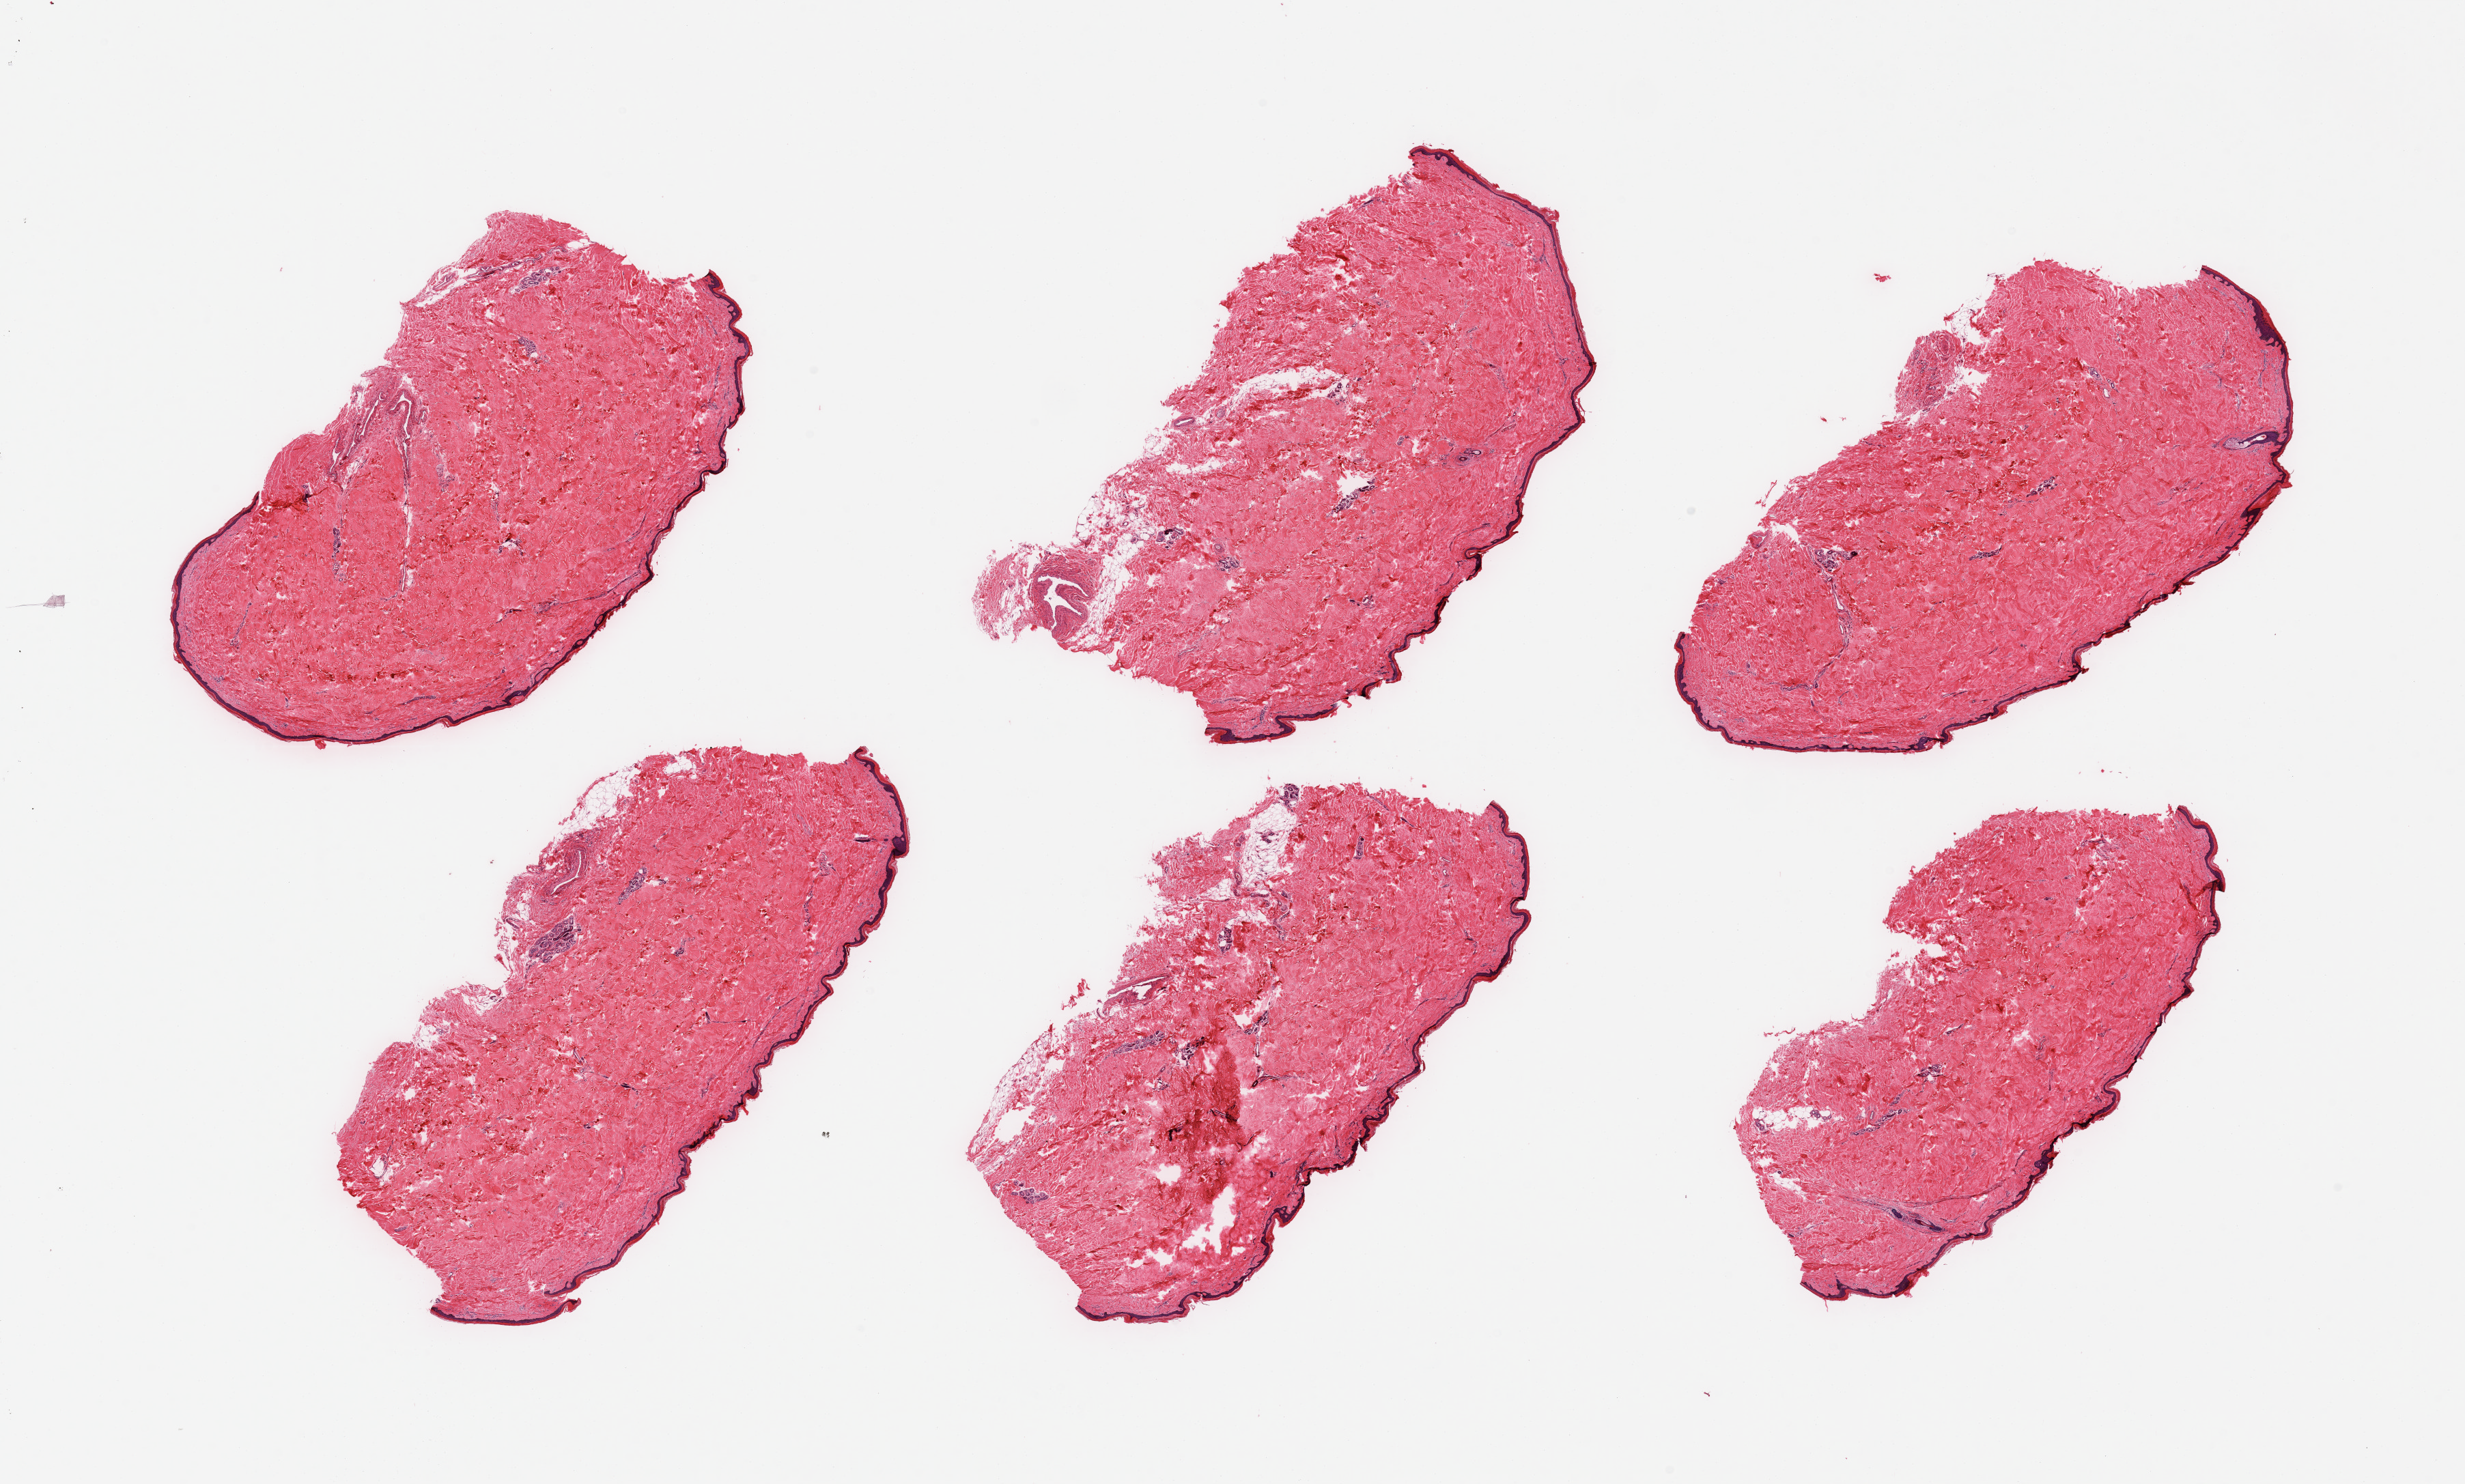
Whole-slide image, haematoxylin and eosin stain — low-resolution overview of the scanned area, about 28.5 x 17.2 mm (slide scanned at 20x). PAXgene-fixed paraffin-embedded (PFPE) section. Target tissue: skin of lower leg. Donor tissue sample.
Reviewer comment on this tissue sample: 6 pieces; well trimmed with minimal internal fat, epidermis measures about 30 microns.